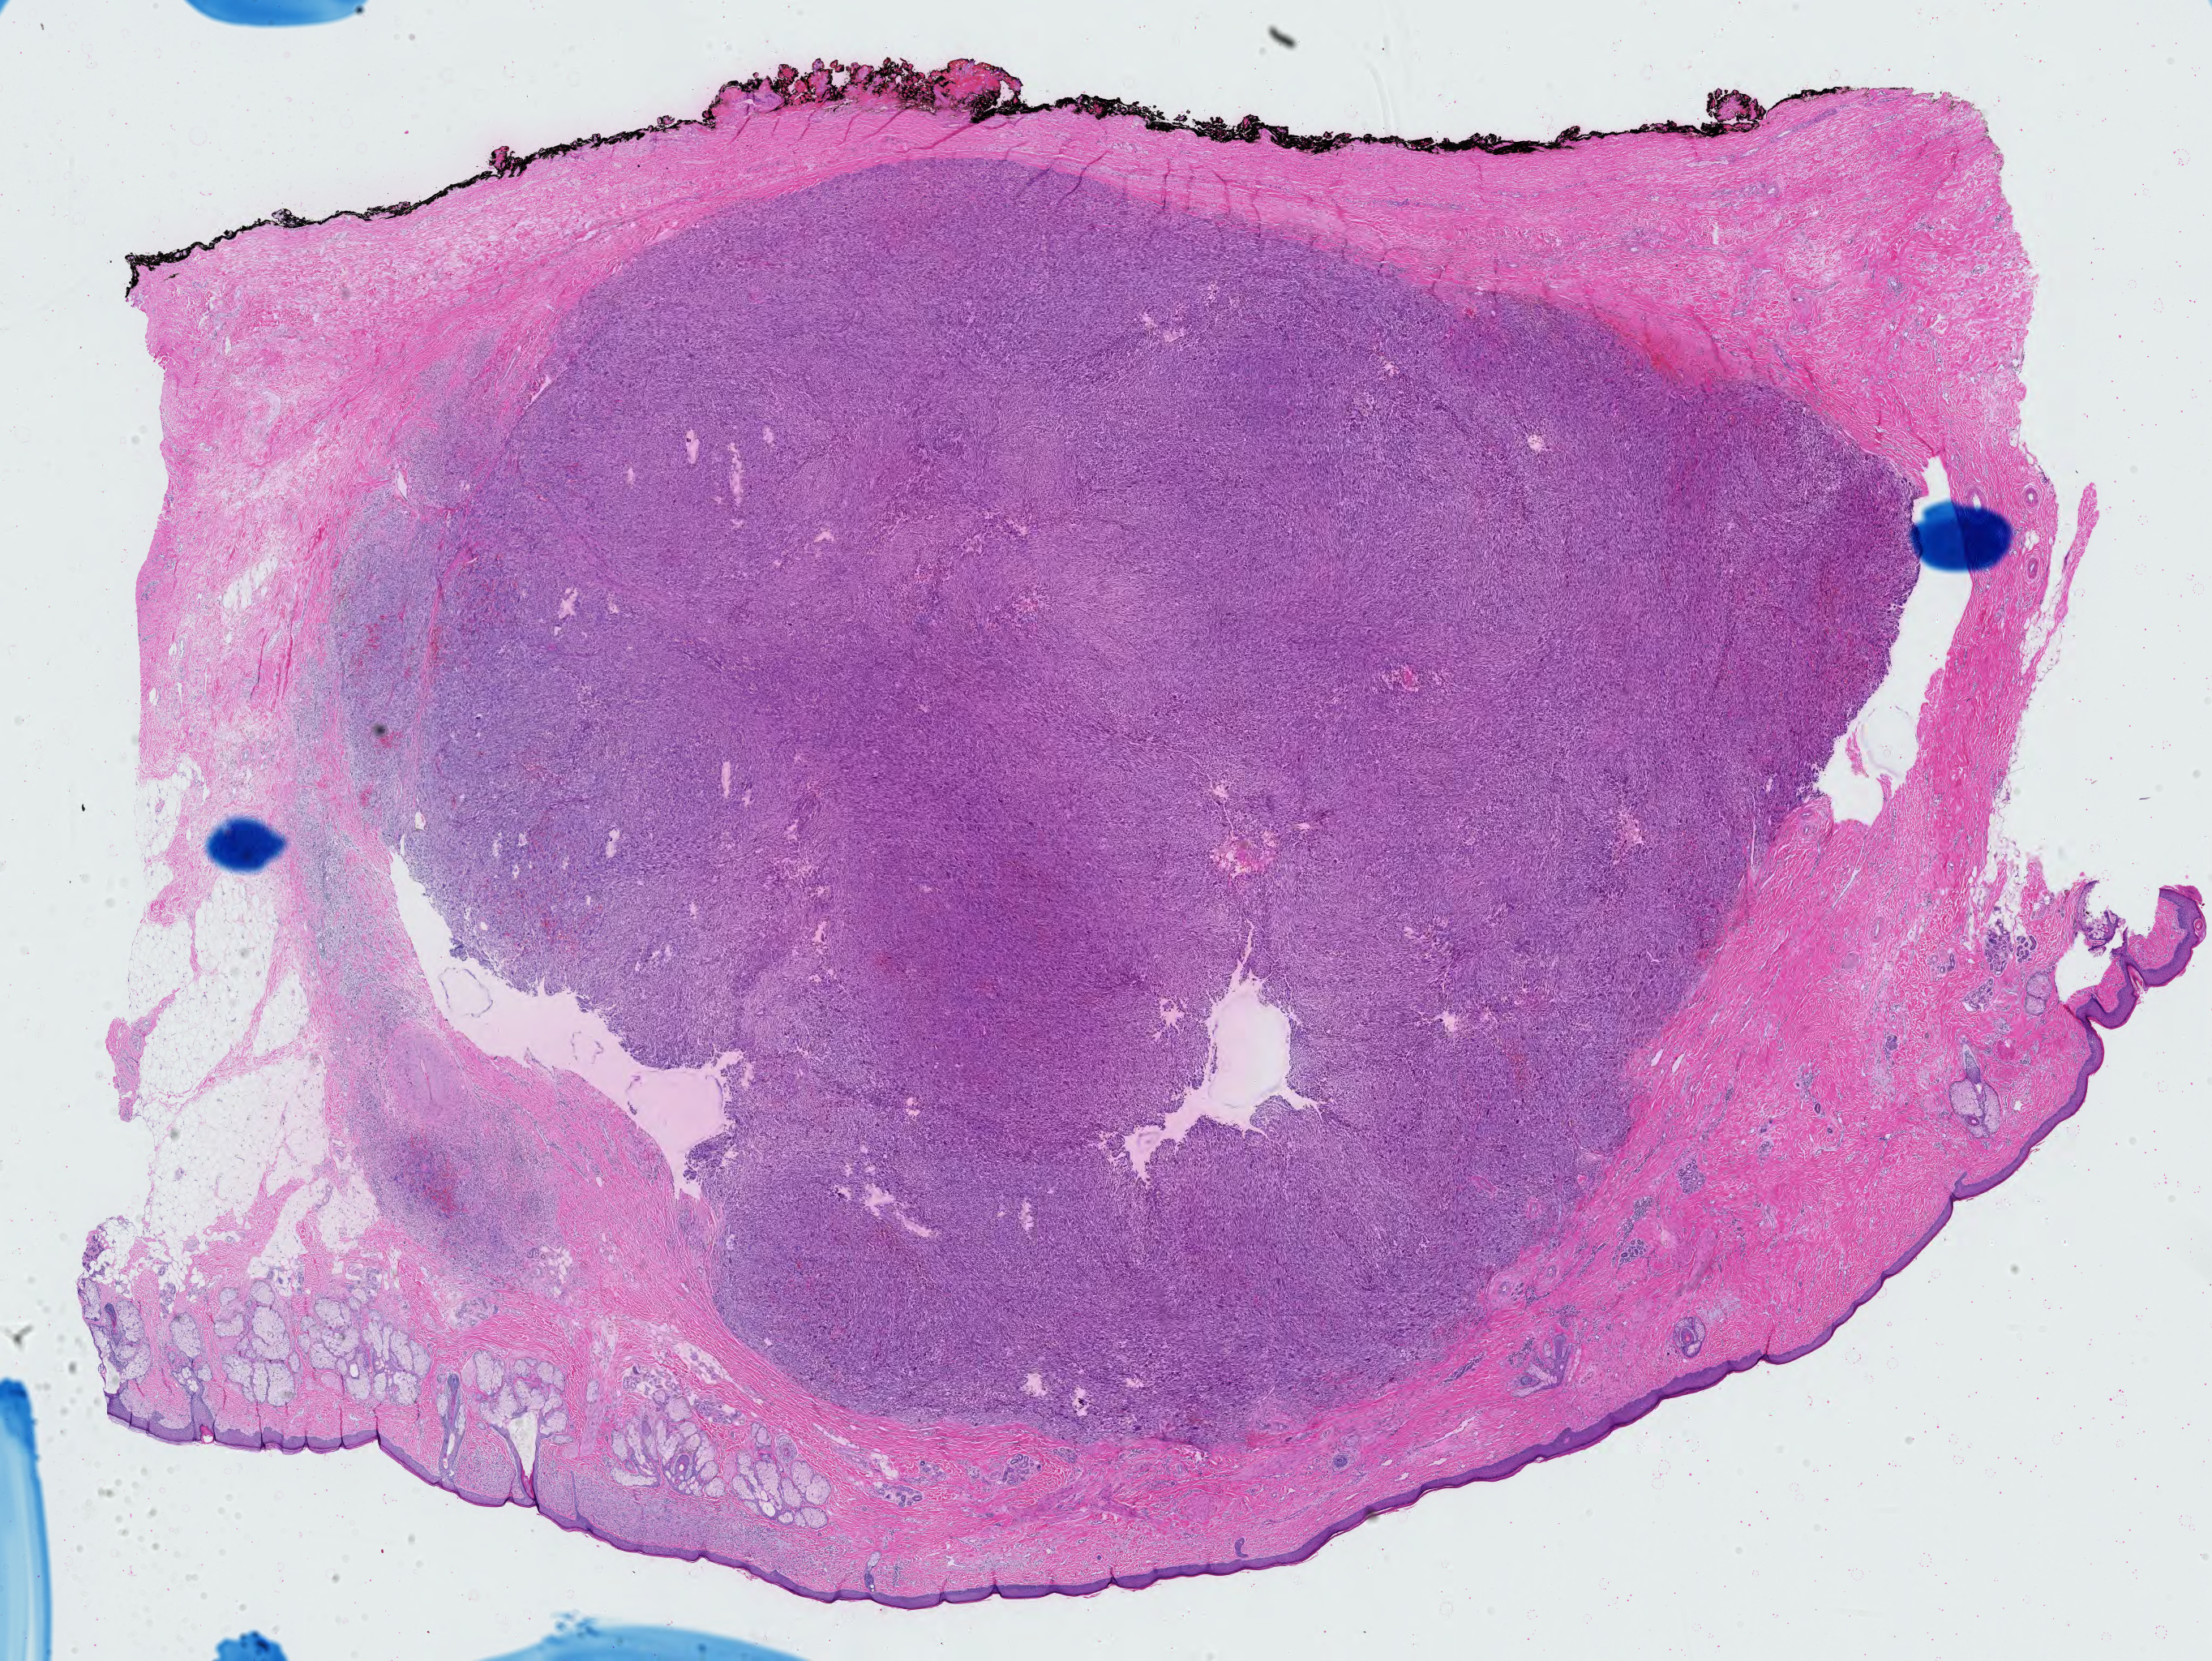
Whole-slide histology image, H&E-stained — low-resolution overview of the scanned area, about 19.8 x 14.8 mm (from a 40x scan); formalin-fixed paraffin-embedded (FFPE) diagnostic section; primary tumour sample from the connective, subcutaneous and other soft tissues. Male patient; age at initial diagnosis 75 years.
Pathologic diagnosis: Undifferentiated sarcoma (connective, subcutaneous and other soft tissues of head, face, and neck).